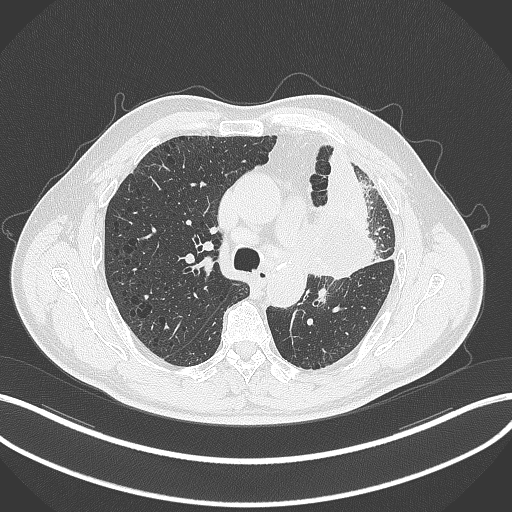
Chest CT, one axial slice. Position 204 of 297 along the scan axis. Lung window (W 1500 / L -600 HU). 1 mm slice thickness. 512 × 512 image matrix, field of view 400 × 400 mm. Male patient, age 68 years. From the clinical record (not read from this slice): clinical TNM (as recorded): T3 N3 M1.
Annotated regions visible in this slice (bounding box drawn by a radiologist):
- lung tumour (recorded histology: adenocarcinoma): box from (x=299, y=189) to (x=380, y=282) px